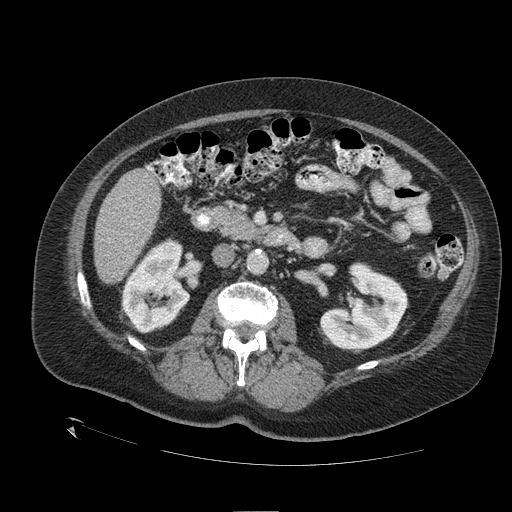
Contrast-enhanced abdominal CT (liver protocol), one axial slice. Position 44 of 109 along the scan axis. One of 2 acquisitions stored at this slice position. Soft-tissue window (W 400 / L 40 HU). 2.5 mm slice thickness. 512 × 512 image matrix, field of view 460 × 460 mm. Case-level facts recorded for this patient, not image findings: diagnosis: hepatocellular carcinoma (patient treated with transarterial chemoembolisation; whether this scan precedes or follows treatment is not stated here); TNM stage (as recorded): Stage-I; Child-Pugh class: A; tumour differentiation: no biopsy; tumour nodularity: uninodular.
Annotated regions visible in this slice (semi-automatic segmentation, software-assisted and operator-edited):
- liver parenchyma outside the tumour (the mass and vessels are separate outlines, so this box may not span the whole liver): bounding box [x1, y1, x2, y2] px = [94, 165, 160, 283]
- liver vessels: [147, 166, 152, 170]